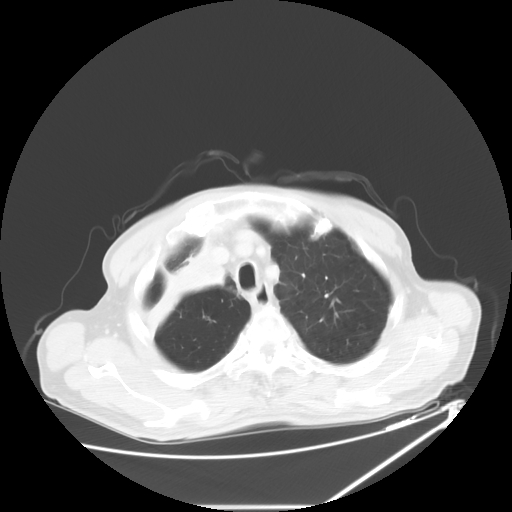
Chest CT, one axial slice. Slice 51 of 60 in the series (ordered by position). 120 kVp. Lung window (W 1500 / L -600 HU). 512 × 512 image matrix, field of view 410 × 410 mm. Male patient, age 73 years. Case-level facts recorded for this patient, not image findings: clinical TNM (as recorded): T2a N1 M0.
Outlined on this slice (rectangle marked by the reading radiologist):
- lung tumour (recorded histology: squamous cell carcinoma): bounding box <128,239,229,341> (left, top, right, bottom; pixels)